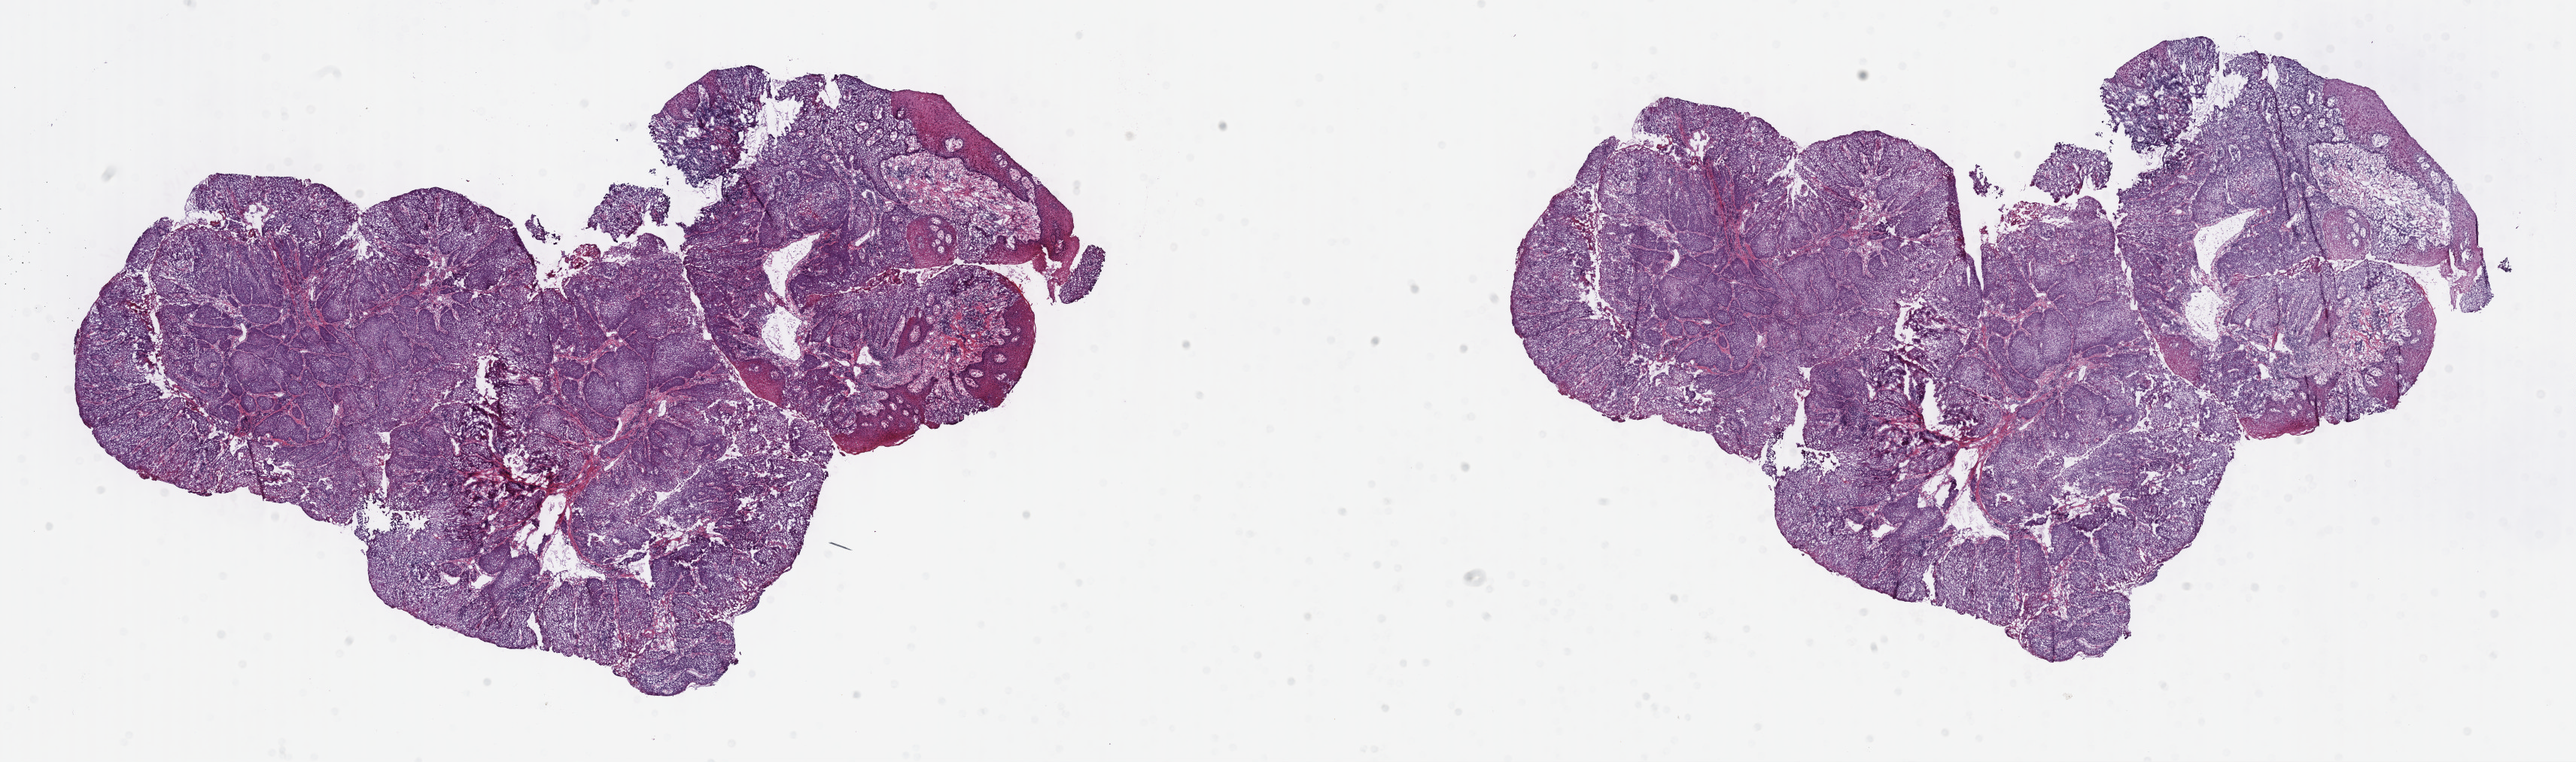
Whole-slide histology image, H&E, whole scanned area (about 27.7 x 8.2 mm, slide scanned at 40x) shown as a low-resolution overview, frozen section, sample: primary tumour, head and neck. Female, age 60 years at initial diagnosis. Histologic grade: G2 (moderately differentiated). Composition of this section per pathologist review: tumour cells 90%, tumour nuclei 90%, normal cells 5%, stromal cells 5%, necrosis 0%. Infiltration values recorded for this section: lymphocyte infiltration 0%, monocyte infiltration 0%, neutrophil infiltration 0%.
* laterality: left
* AJCC pathologic stage: IVC (7th edition)
* histologic diagnosis: Squamous cell carcinoma, NOS (larynx, NOS)
* TNM: T3 N1 M1